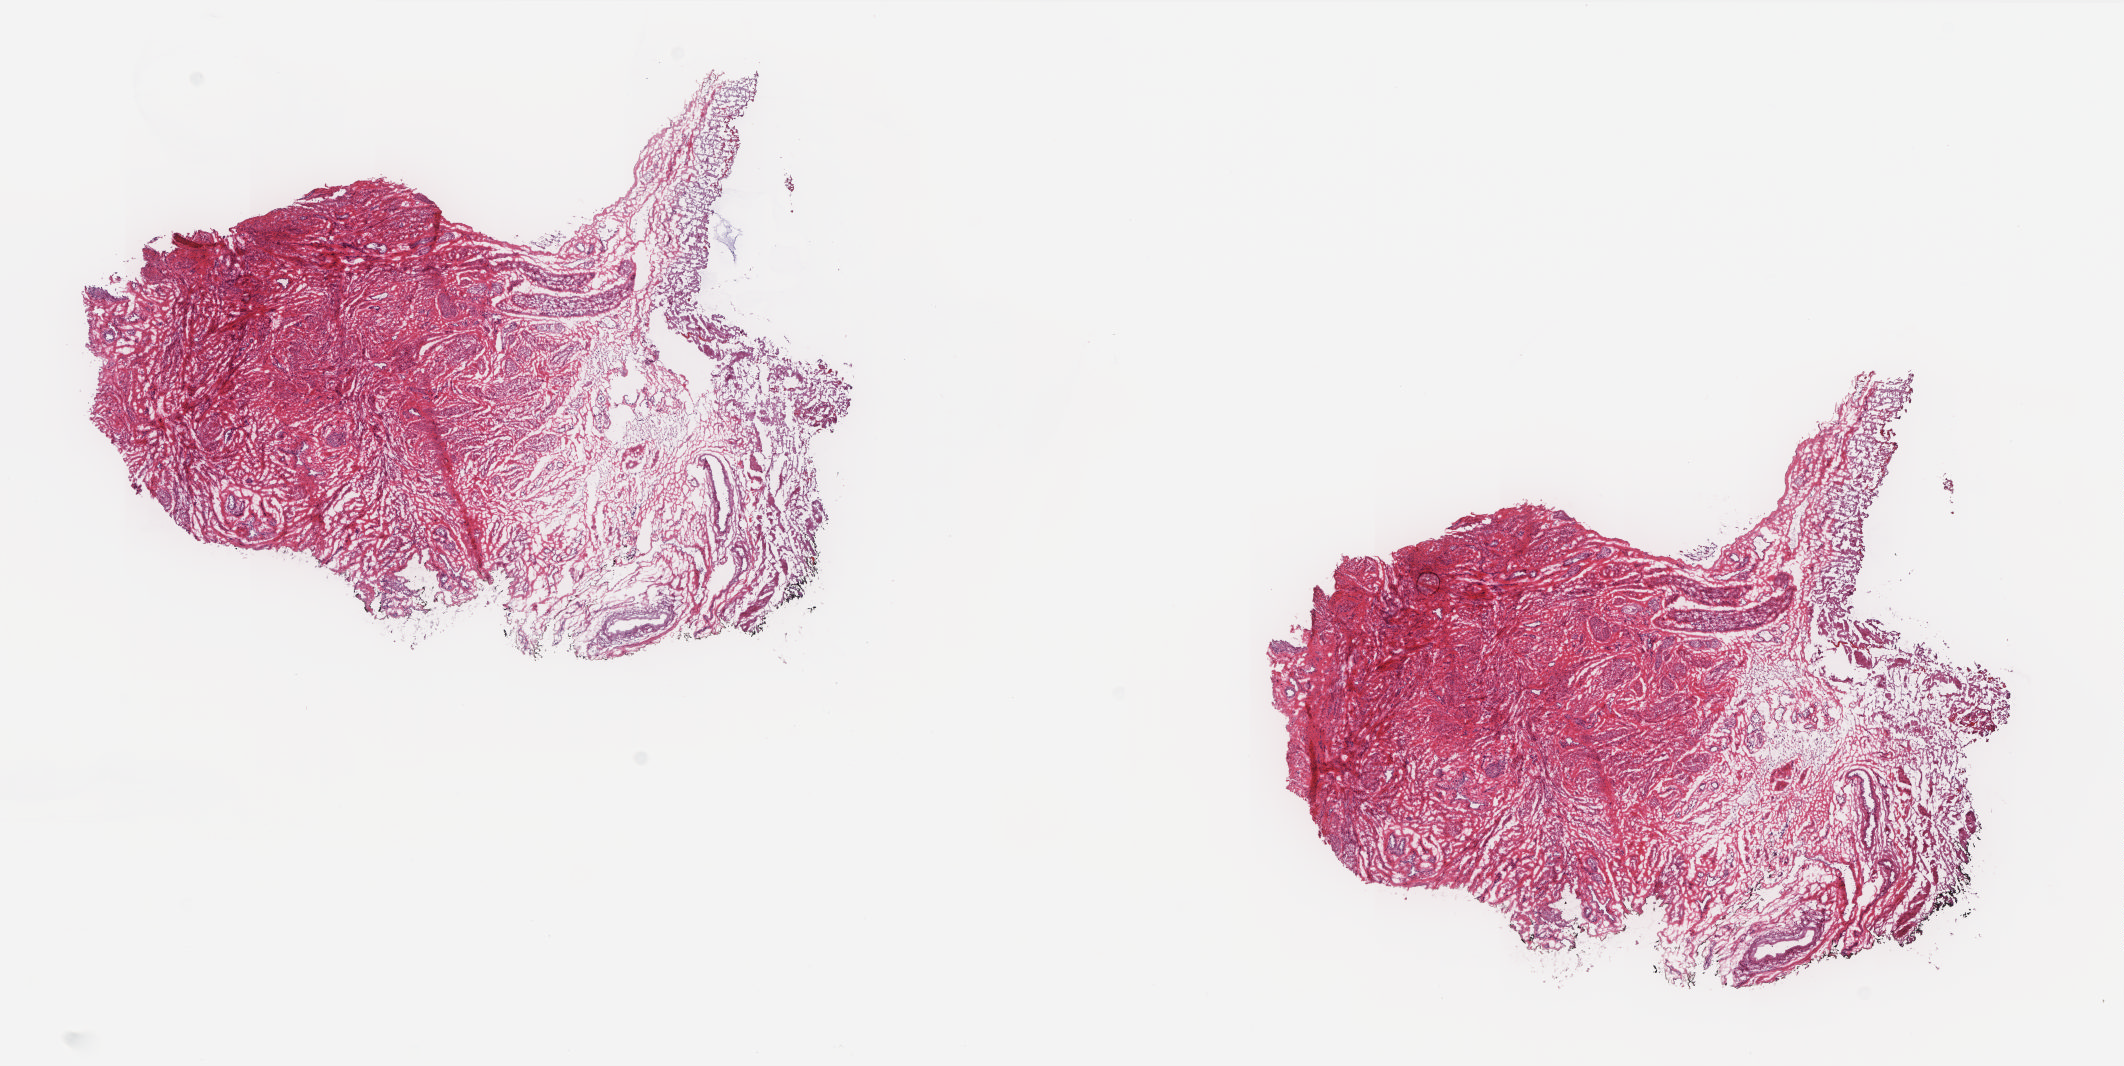
H&E whole-slide image, low-resolution overview of the scanned area, about 17.0 x 8.5 mm. Frozen section from the top of the tissue portion. Solid tissue normal (non-tumour tissue) sample from the uterus. Female patient; age at initial diagnosis 53 years. Slide review estimates, as recorded: tumour cells 0%, tumour nuclei 0%.
This section: solid tissue normal sample (biorepository sample class). Patient diagnosis: Serous cystadenocarcinoma, NOS.